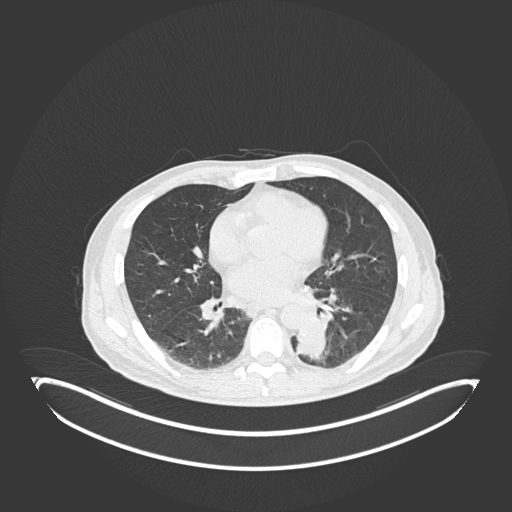
Chest CT, one axial slice; position 82 of 251 along the scan axis; reconstruction kernel B30f; lung window (W 1500 / L -600 HU); 1 mm slice thickness; 512 × 512 image matrix. Male patient, age 72 years. From the clinical record (not read from this slice): clinical TNM (as recorded): T2b N0 M1.
Outlined on this slice (rectangle marked by the reading radiologist):
- lung tumour (recorded histology: adenocarcinoma): bounding box <294,307,331,359> (left, top, right, bottom; pixels)